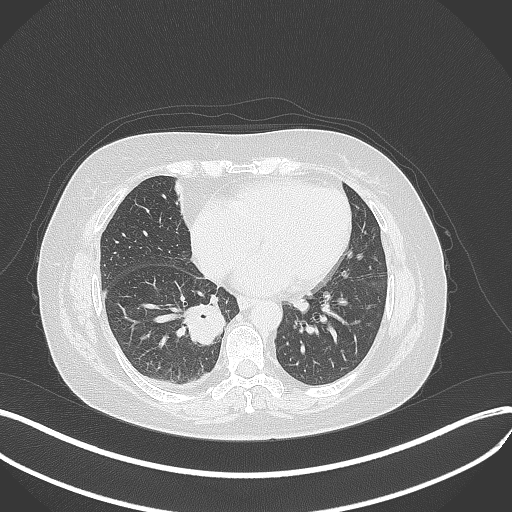
Chest CT, one axial slice; position 136 of 381 along the scan axis; 120 kVp; lung window (W 1500 / L -600 HU); 1 mm slice thickness; 512 × 512 image matrix. Female patient, age 56 years. Case-level facts recorded for this patient, not image findings: clinical TNM (as recorded): T2b N1 M0; histopathological grade: G3.
Outlined on this slice (rectangle marked by the reading radiologist):
- lung tumour (recorded histology: small cell carcinoma): bounding box (x1, y1, x2, y2) in pixels: (186, 303, 225, 350)